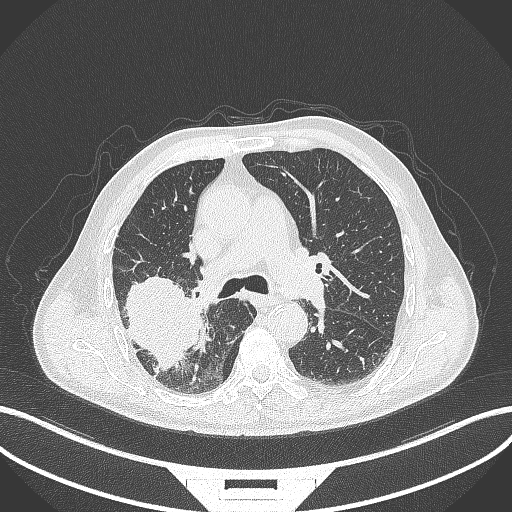
Chest CT, one axial slice. Position 255 of 429 along the scan axis. Reconstruction kernel B70f. Lung window (W 1500 / L -600 HU). 1 mm slice thickness. 512 × 512 image matrix, field of view 400 × 400 mm. Patient: male, 72 years. From the clinical record (not read from this slice): clinical TNM (as recorded): T3 N2 M0.
Structures marked on this image (bounding box drawn by a radiologist):
- lung tumour (recorded histology: adenocarcinoma): bounding box <118,273,207,372> (left, top, right, bottom; pixels)